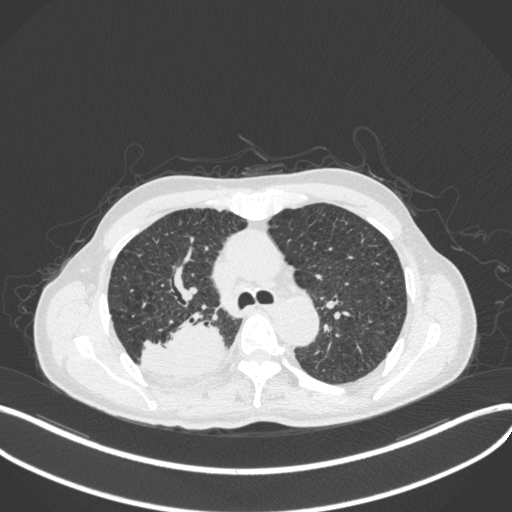
Chest CT, one axial slice. Position 308 of 423 along the scan axis. Lung window (W 1500 / L -600 HU). 1 mm slice thickness. 512 × 512 image matrix. Male patient, age 79 years. From the clinical record (not read from this slice): clinical TNM (as recorded): T3 N0 M0.
Outlined on this slice (rectangle marked by the reading radiologist):
- lung tumour (recorded histology: adenocarcinoma): box from (x=140, y=309) to (x=228, y=381) px